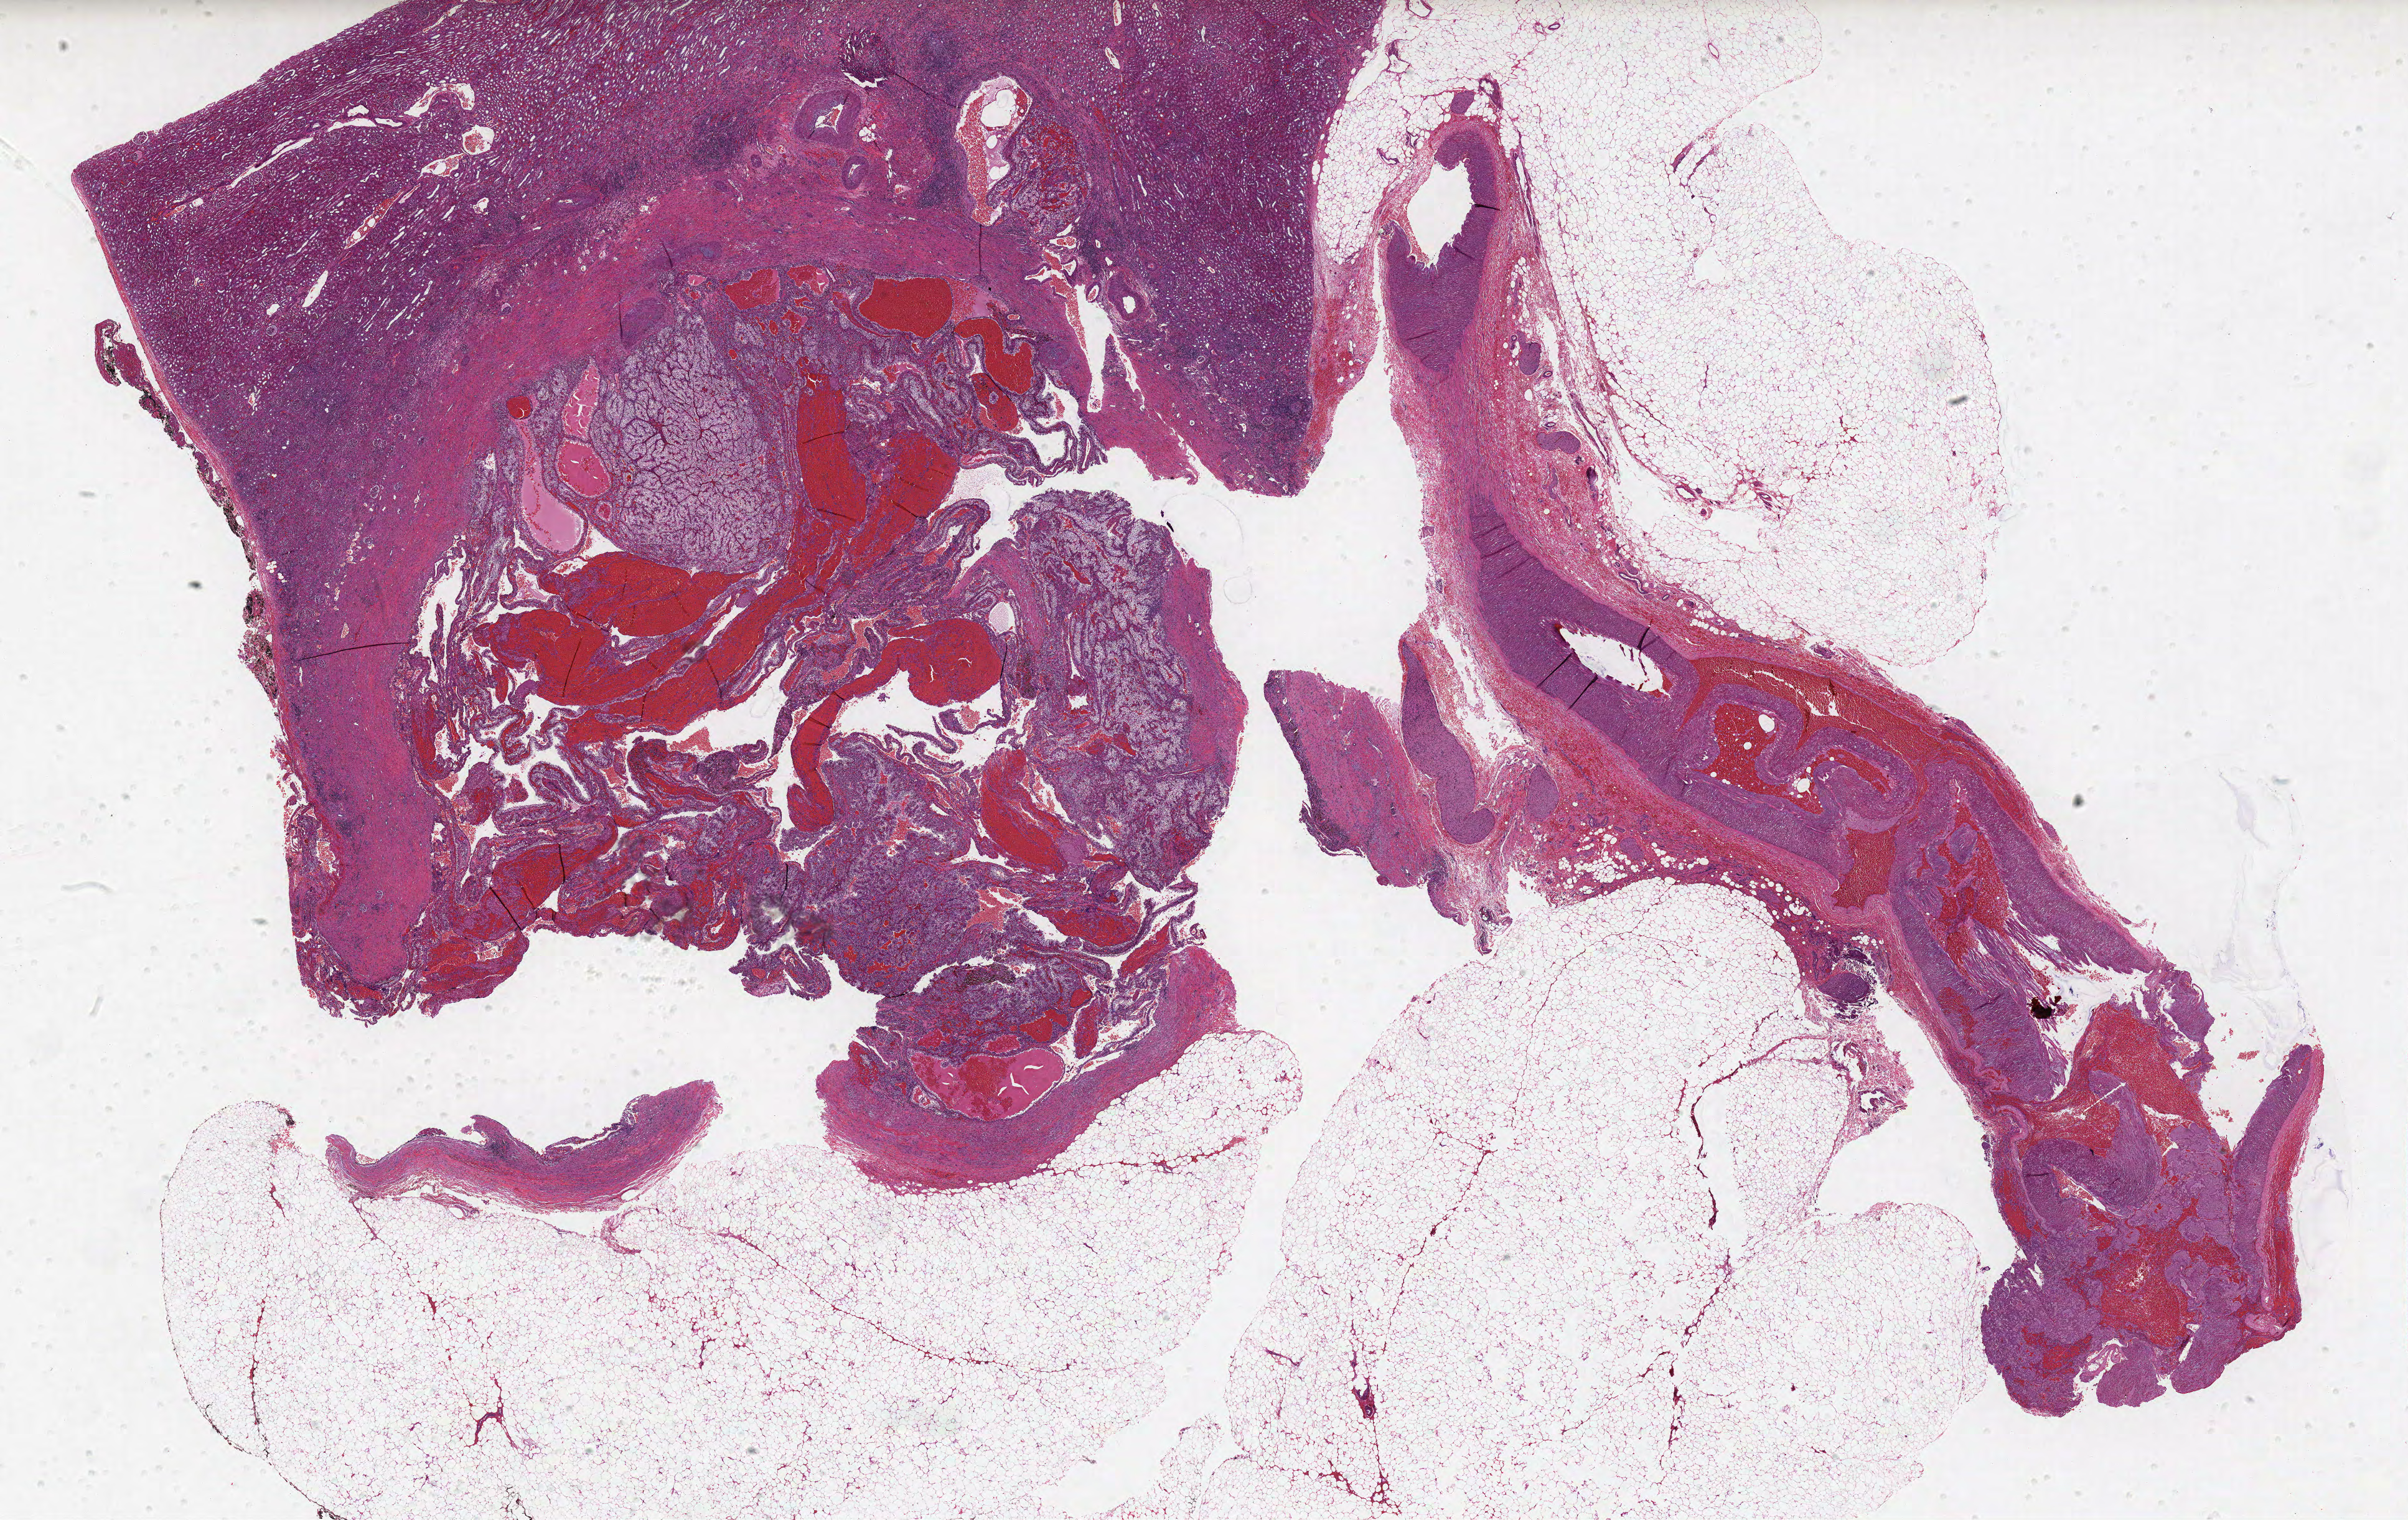
H&E whole-slide image — low-resolution overview of the scanned area, about 30.9 x 19.5 mm. Formalin-fixed paraffin-embedded (FFPE) diagnostic section. Sample: primary tumour, kidney. Male, age 46 years at initial diagnosis.
Pathologic diagnosis: Clear cell adenocarcinoma, NOS.